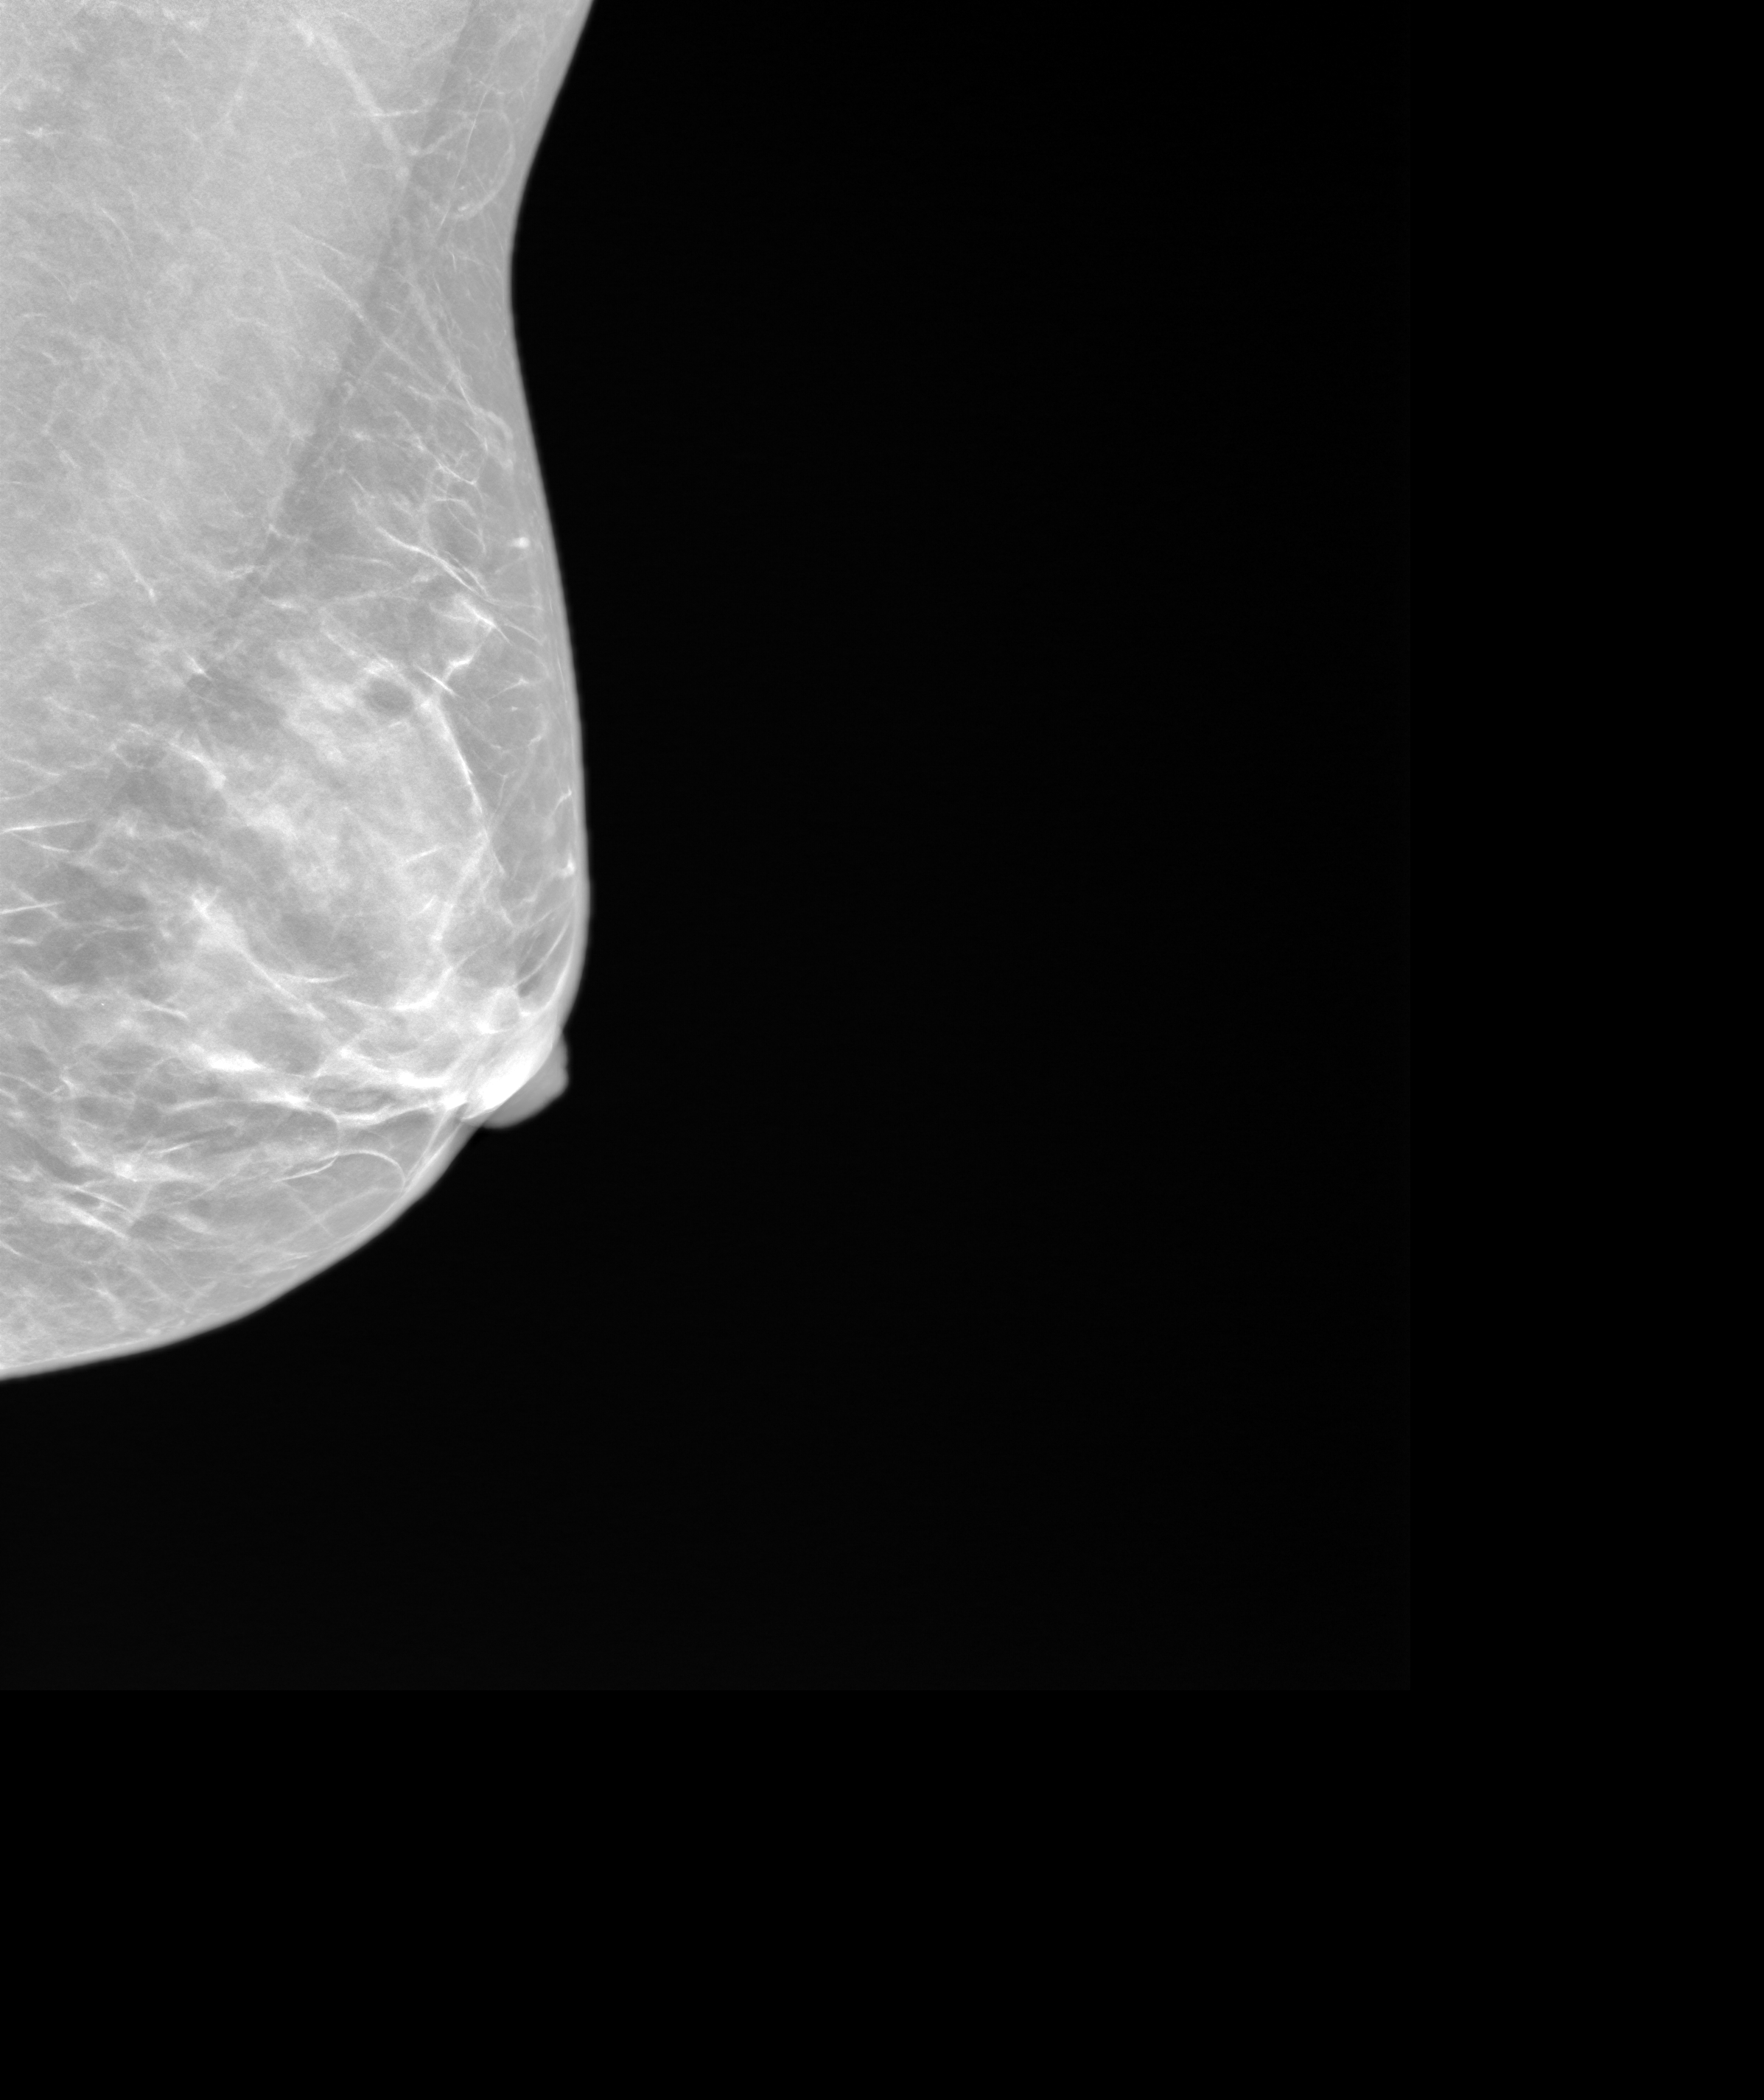
Synthetic 2-D view generated from a tomosynthesis acquisition (not an FFDM exposure); left breast; medio-lateral oblique projection; screening examination; system: SenoIris_1SP1.1(421). Patient aged 48 years (female).
BI-RADS breast density category at the screening exam (both breasts, scale 1–4): 3. Final BI-RADS assessment for this screening round (tomosynthesis exam, both breasts): category 2. Recall: no recall after this screen.